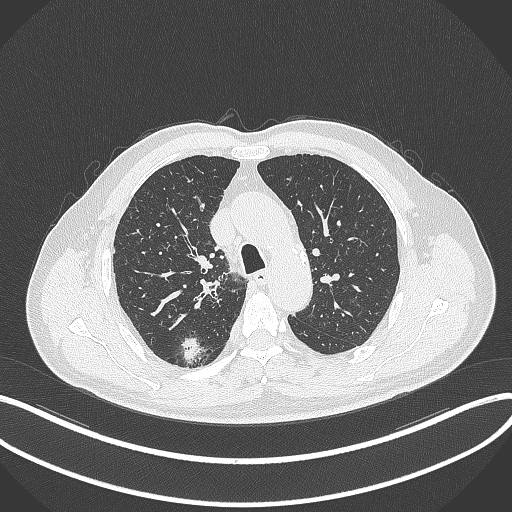
Chest CT, one axial slice. Slice 267 of 359 in the series (ordered by position). Reconstruction kernel B70f. 120 kVp. Lung window (W 1500 / L -600 HU). 1 mm slice thickness. 512 × 512 image matrix, field of view 400 × 400 mm. Patient: male, 69 years. Case-level facts recorded for this patient, not image findings: clinical TNM (as recorded): T1b N0 M0; histopathological grade: G2-3.
Annotated regions visible in this slice (bounding box drawn by a radiologist):
- lung tumour (recorded histology: adenocarcinoma): bounding box <178,334,206,366> (left, top, right, bottom; pixels)